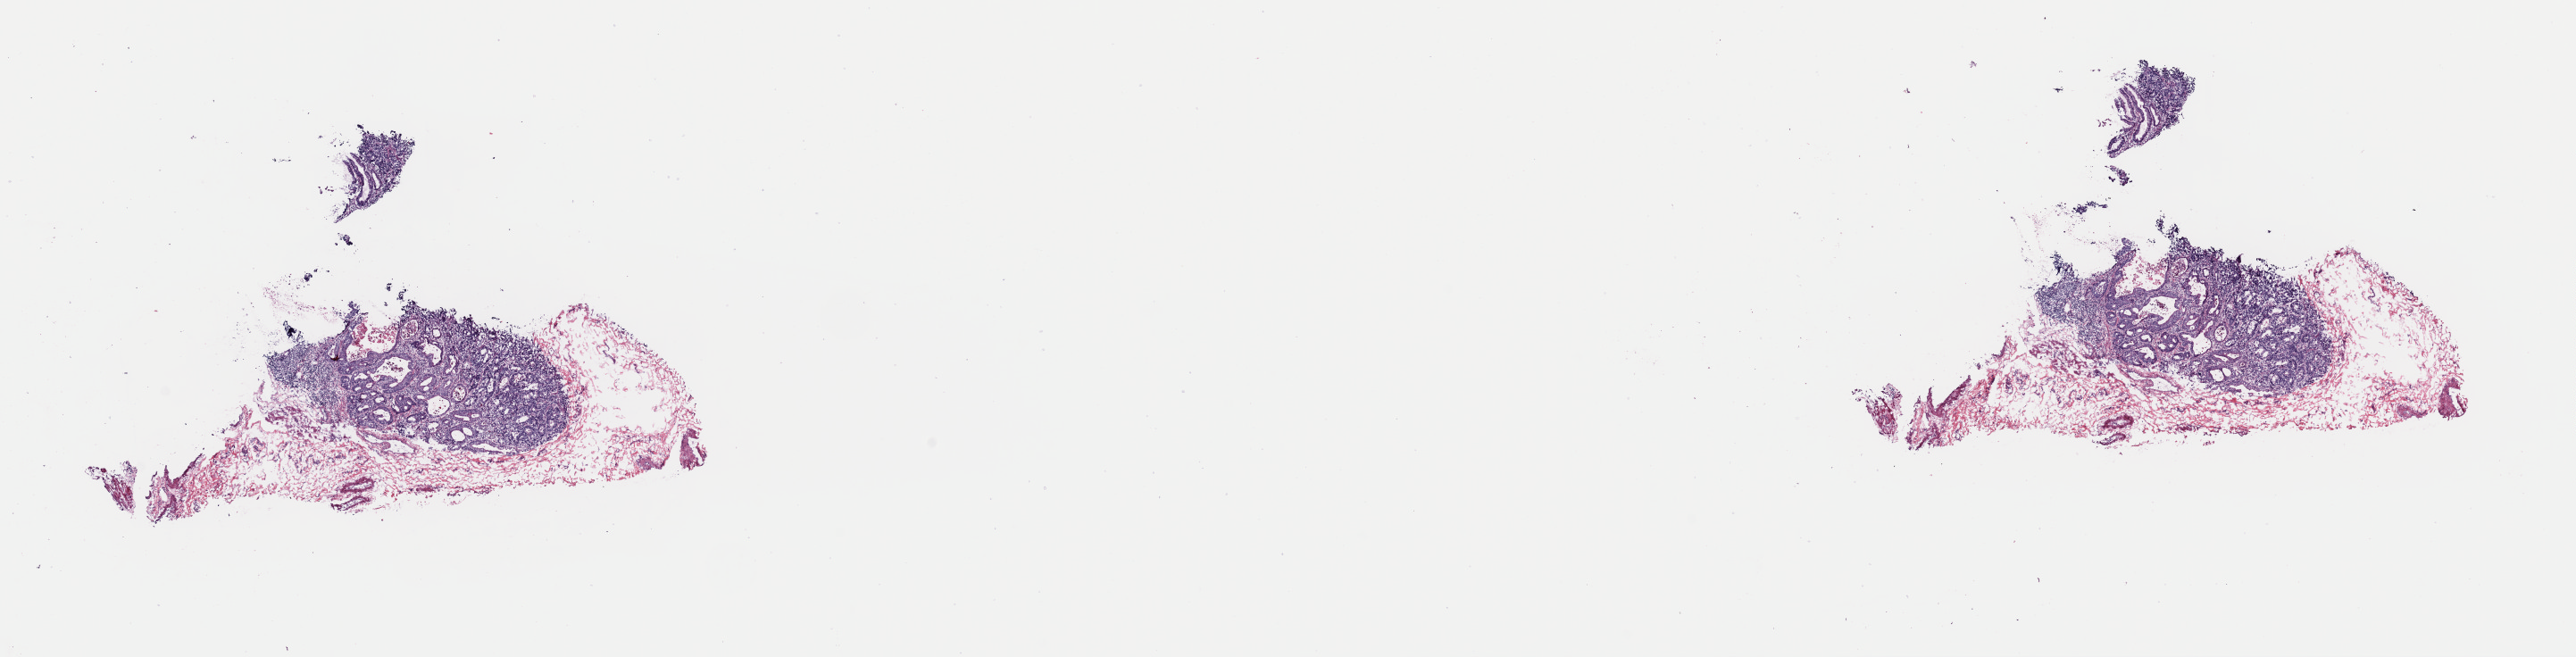
Digitized H&E-stained tissue section (whole slide) — whole scanned area (about 22.8 x 5.8 mm) shown as a low-resolution overview, frozen section from the top of the tissue portion, sample: primary tumour, esophagus. Patient: male, age at initial diagnosis 59 years. Pathologist review of this section (percent, as recorded): tumour cells 30%, tumour nuclei 65%.
Histologic diagnosis: Adenocarcinoma, NOS (lower third of esophagus).